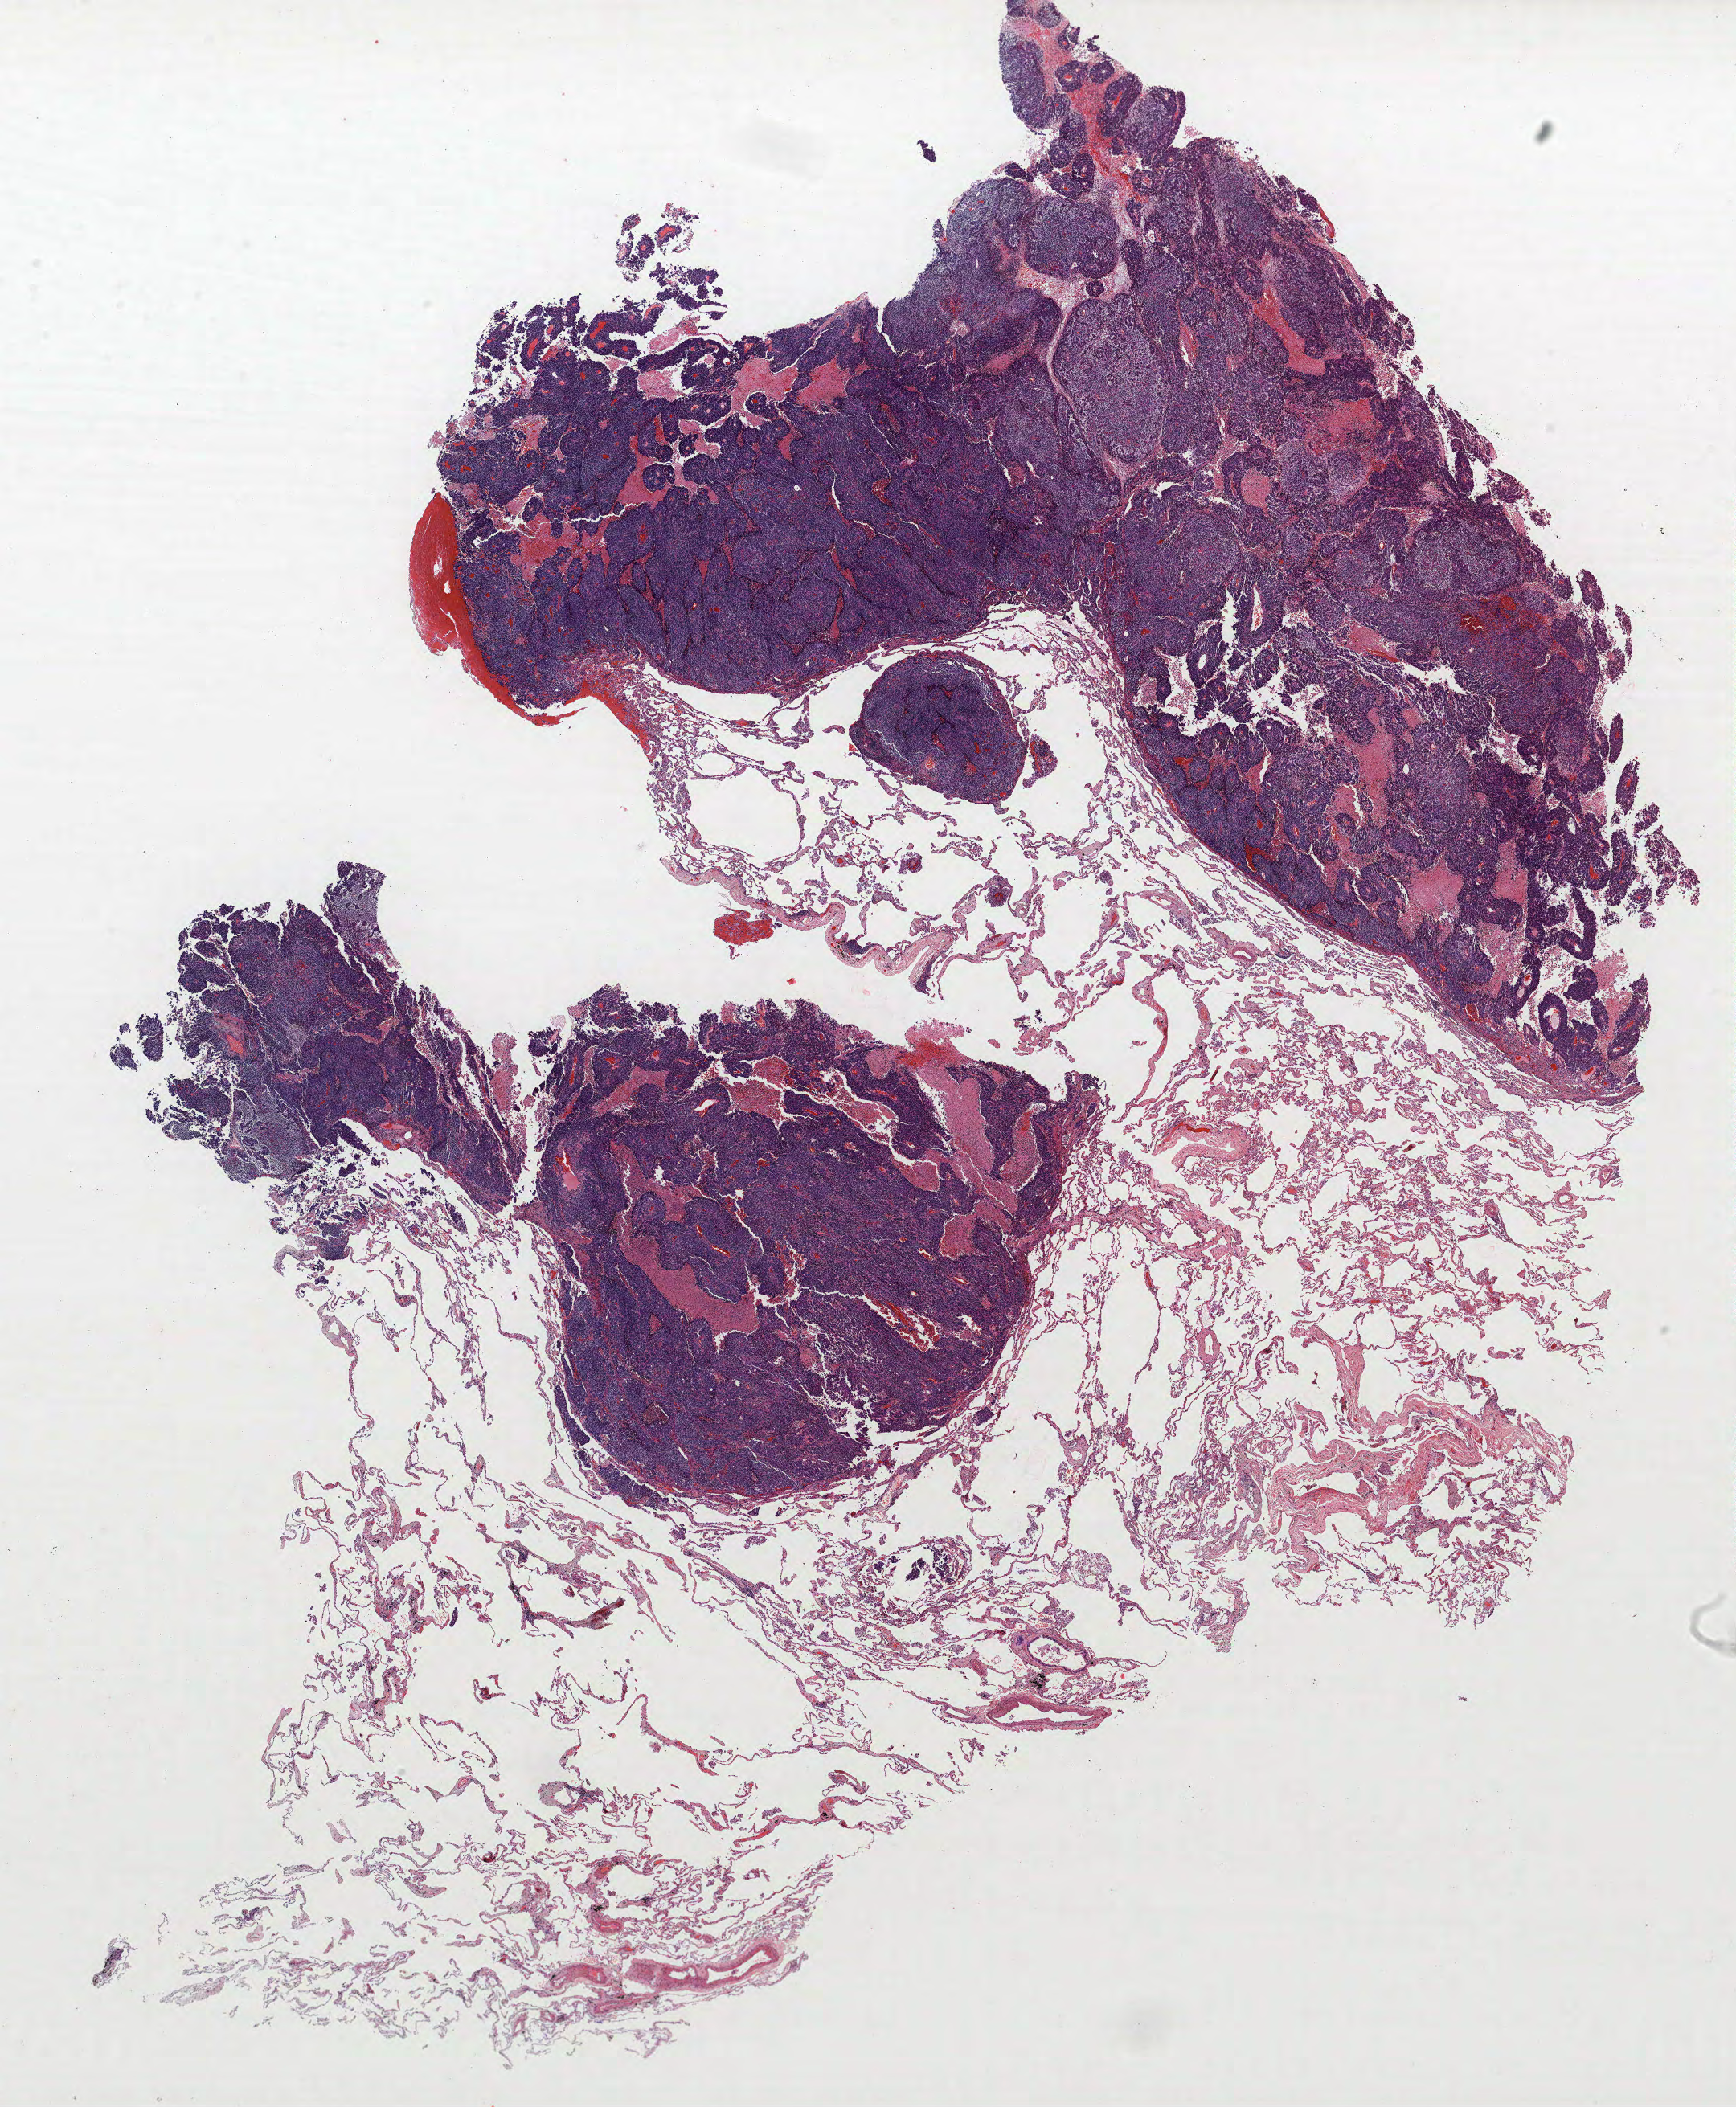
Whole-slide histology image, H&E-stained, low-resolution overview of the scanned area, about 17.3 x 21.0 mm. FFPE section. Lung. Female, age 70 at enrolment. Former smoker at enrolment.
Participant's lung-cancer diagnosis: Large cell neuroendocrine carcinoma (ICD-O-3 8013/3).